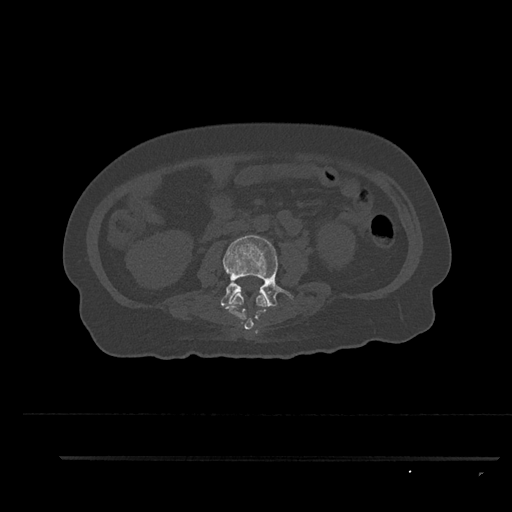
CT including the spine, one axial slice; slice 109 of 797 in the series (ordered by position); reconstruction kernel Br40s/3; 120 kVp; bone window (W 1800 / L 400 HU); 512 × 512 image matrix. Patient: female, 44 years. Case-level facts recorded for this patient, not image findings: primary cancer: renal; vertebrae with lytic lesions (as recorded): L1.
Structures marked on this image (semi-automatic segmentation, software-assisted and operator-edited):
- L2 vertebra: bounding box <226,293,266,330> (left, top, right, bottom; pixels)
- L3 vertebra: <220,235,293,311>